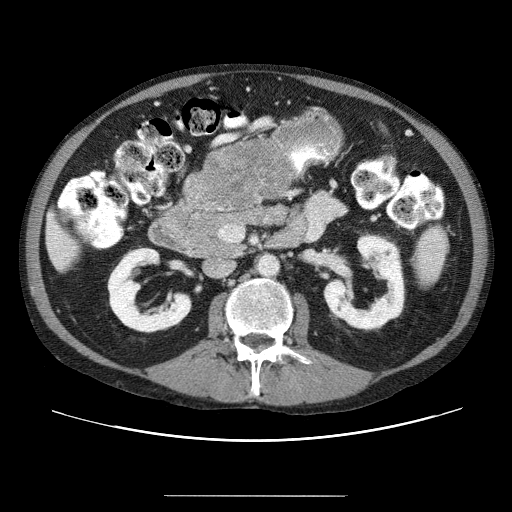
Contrast-enhanced abdominal CT (liver protocol), one axial slice; slice 3 of 69 in the series (ordered by position); 120 kVp; soft-tissue window (W 400 / L 40 HU); 2.5 mm slice thickness; 512 × 512 image matrix. From the clinical record (not read from this slice): diagnosis: hepatocellular carcinoma (patient treated with transarterial chemoembolisation; whether this scan precedes or follows treatment is not stated here); TNM stage (as recorded): Stage-IVB; Child-Pugh class: B.
Outlined on this slice (semi-automatically segmented with operator editing):
- liver parenchyma outside the tumour (the mass and vessels are separate outlines, so this box may not span the whole liver): bounding box (x1, y1, x2, y2) in pixels: (46, 216, 70, 268)
- mass: (201, 142, 288, 210)